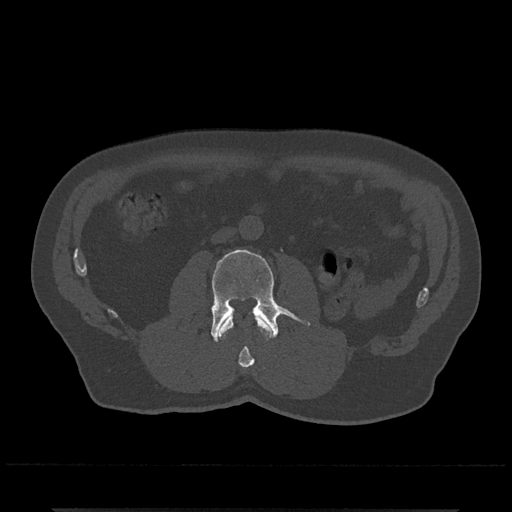
CT including the spine, one axial slice; position 241 of 797 along the scan axis; reconstruction kernel Br40s/3; 120 kVp; bone window (W 1800 / L 400 HU); 0.5 mm slice thickness; 512 × 512 image matrix, field of view 393 × 393 mm. Patient: male, 67 years. Case-level facts recorded for this patient, not image findings: primary cancer: prostate.
Annotated regions visible in this slice (semi-automatically segmented with operator editing):
- L2 vertebra: bounding box [x1, y1, x2, y2] px = [219, 315, 271, 368]
- L3 vertebra: [211, 249, 310, 342]